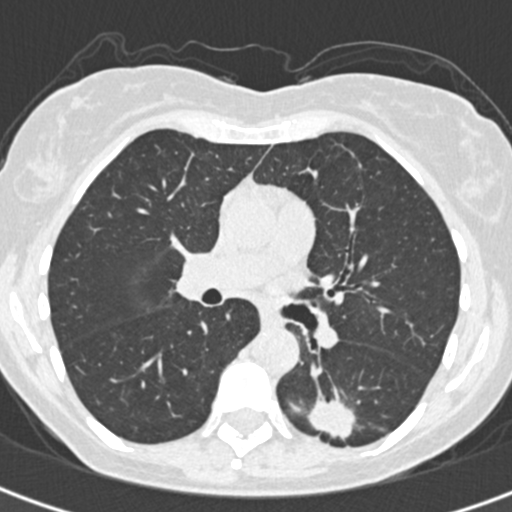
Low-dose screening chest CT, one axial slice. Reconstruction kernel B30f. 120 kVp. Lung window (W 1500 / L -600 HU). 1 mm slice thickness. 512 × 512 image matrix, field of view 284 × 284 mm.
Outlined on this slice (manually delineated by an expert):
- lesion 1 (tumor, lower lobe of left lung): bounding box <307,398,356,439> (left, top, right, bottom; pixels)